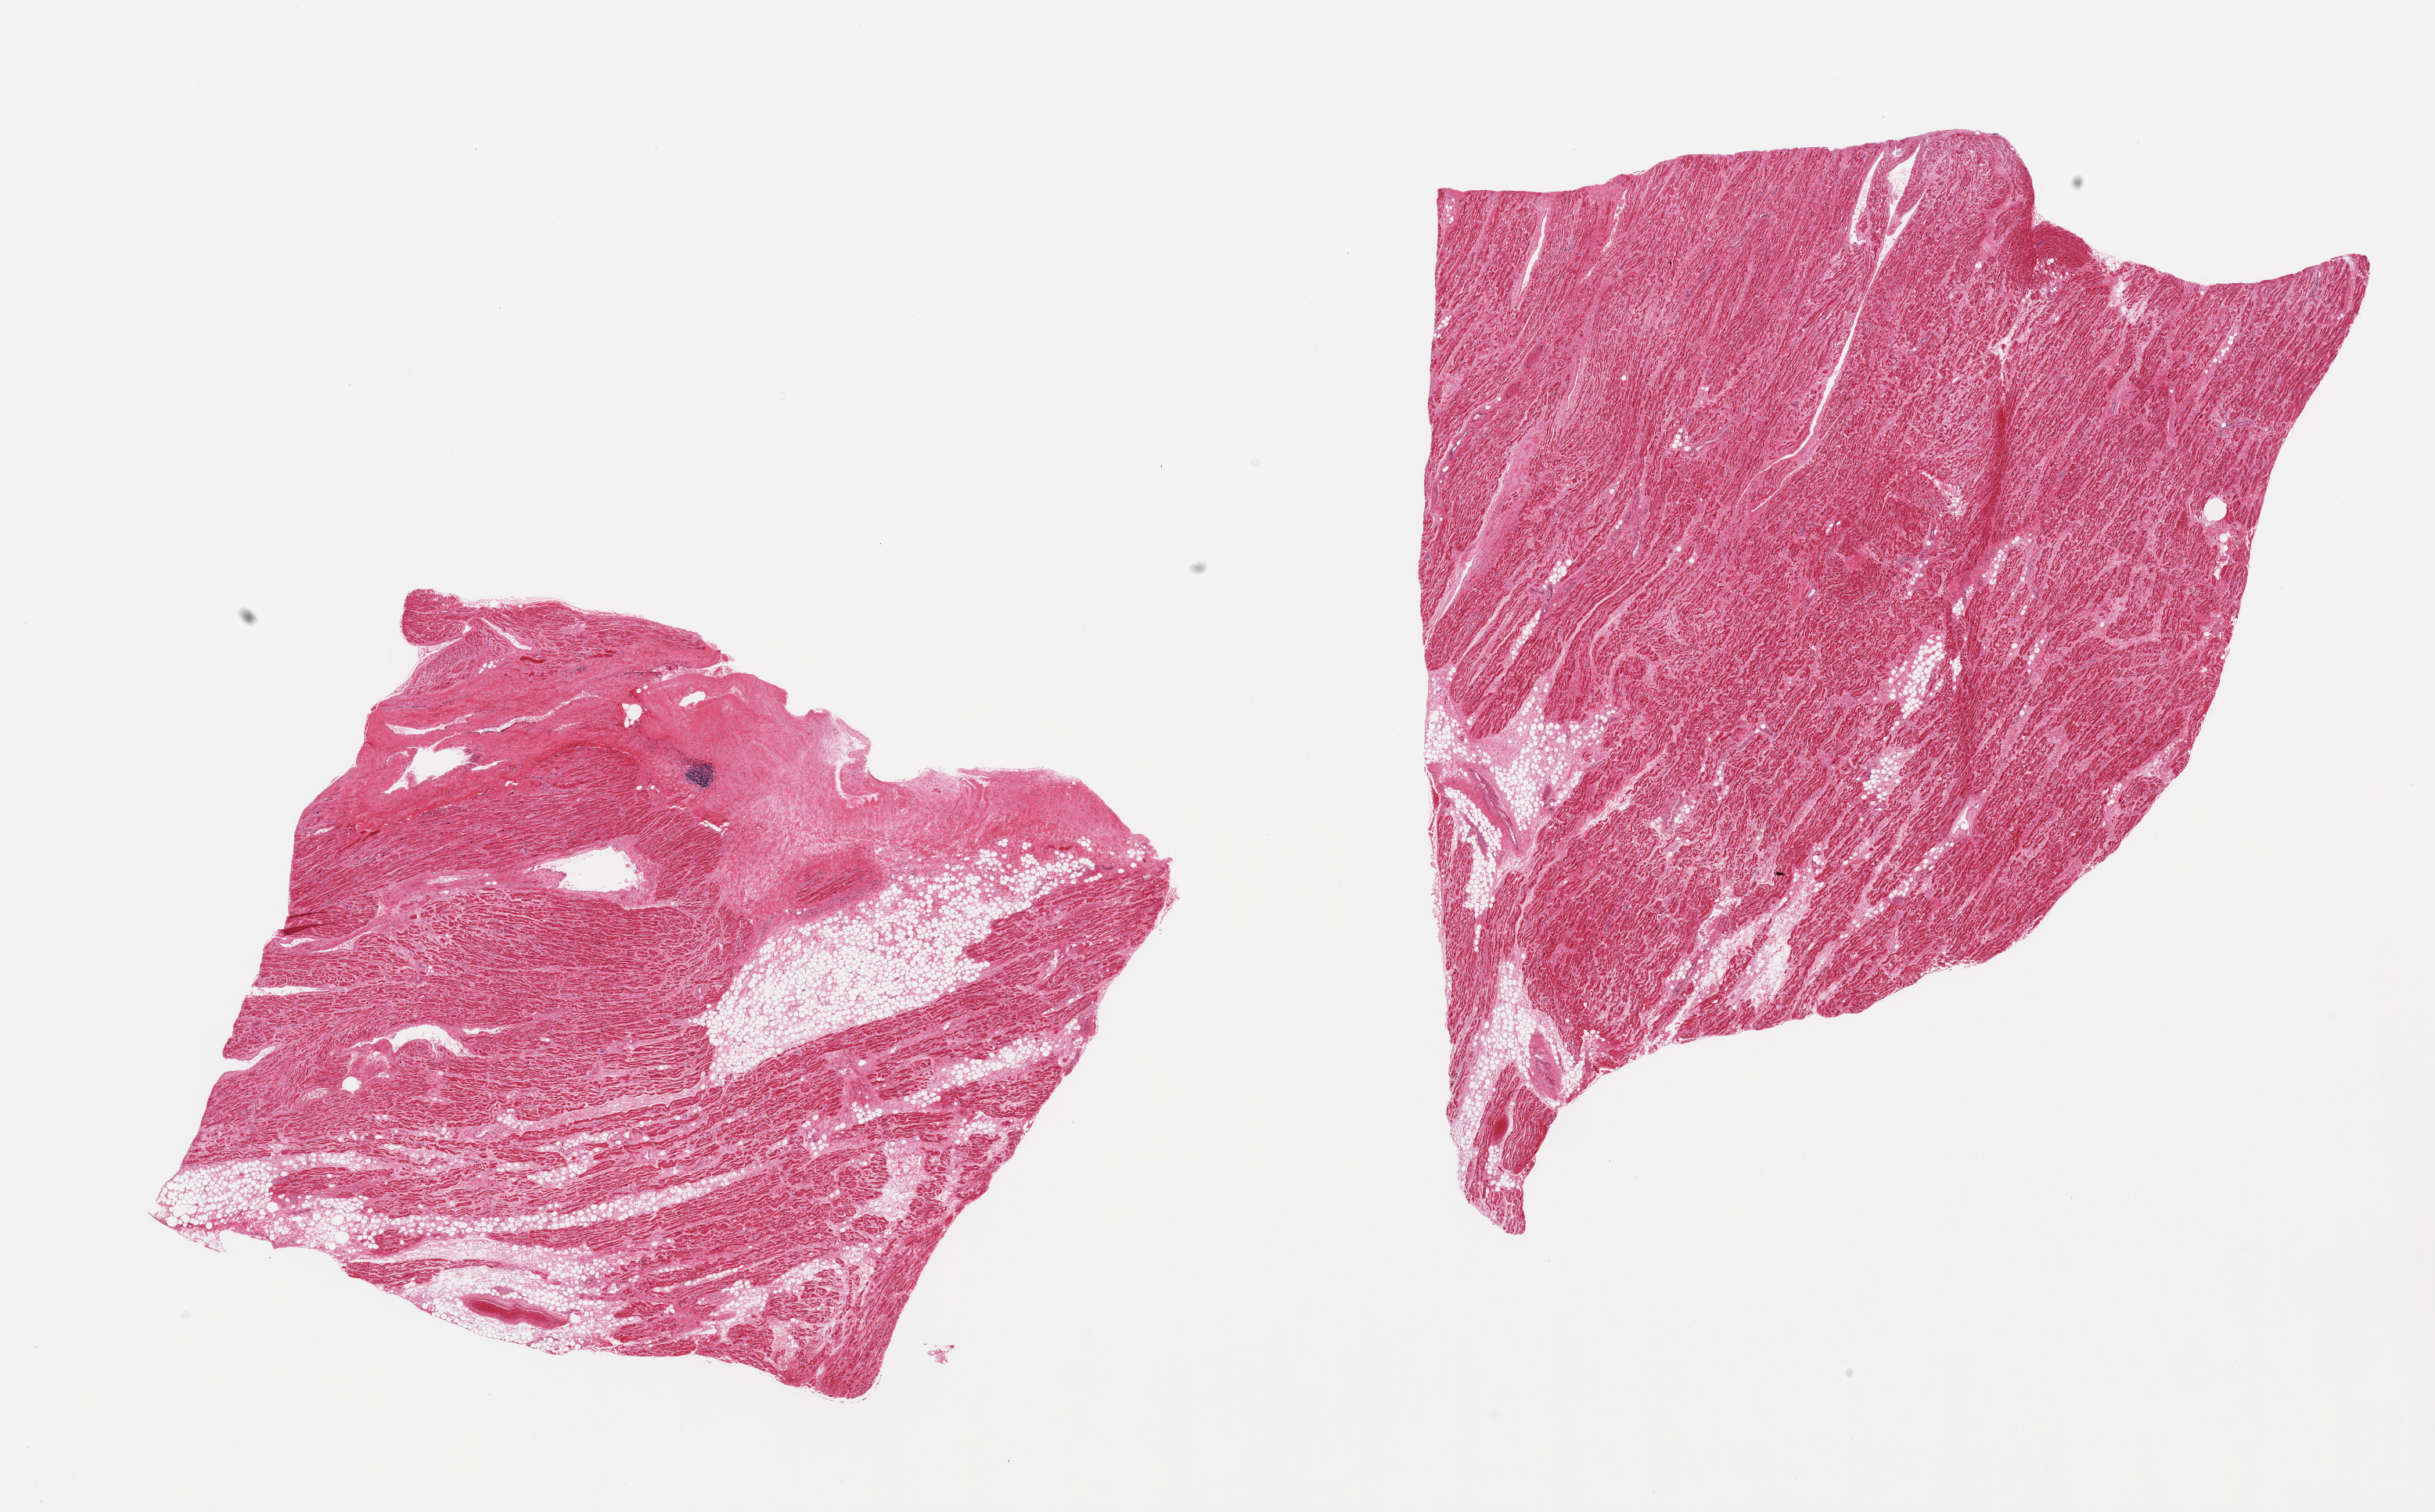
Digitized hematoxylin and eosin (H&E)-stained section — a low-resolution overview of the entire scanned area, about 24.6 x 15.3 mm (from a 20x scan). PAXgene-fixed paraffin-embedded (PFPE) section. Target tissue: auricular appendage. Tissue donor sample. Donor sex: male.
- reviewer comment on this tissue sample: 2 pieces; 50% & 20% fibrofatty content